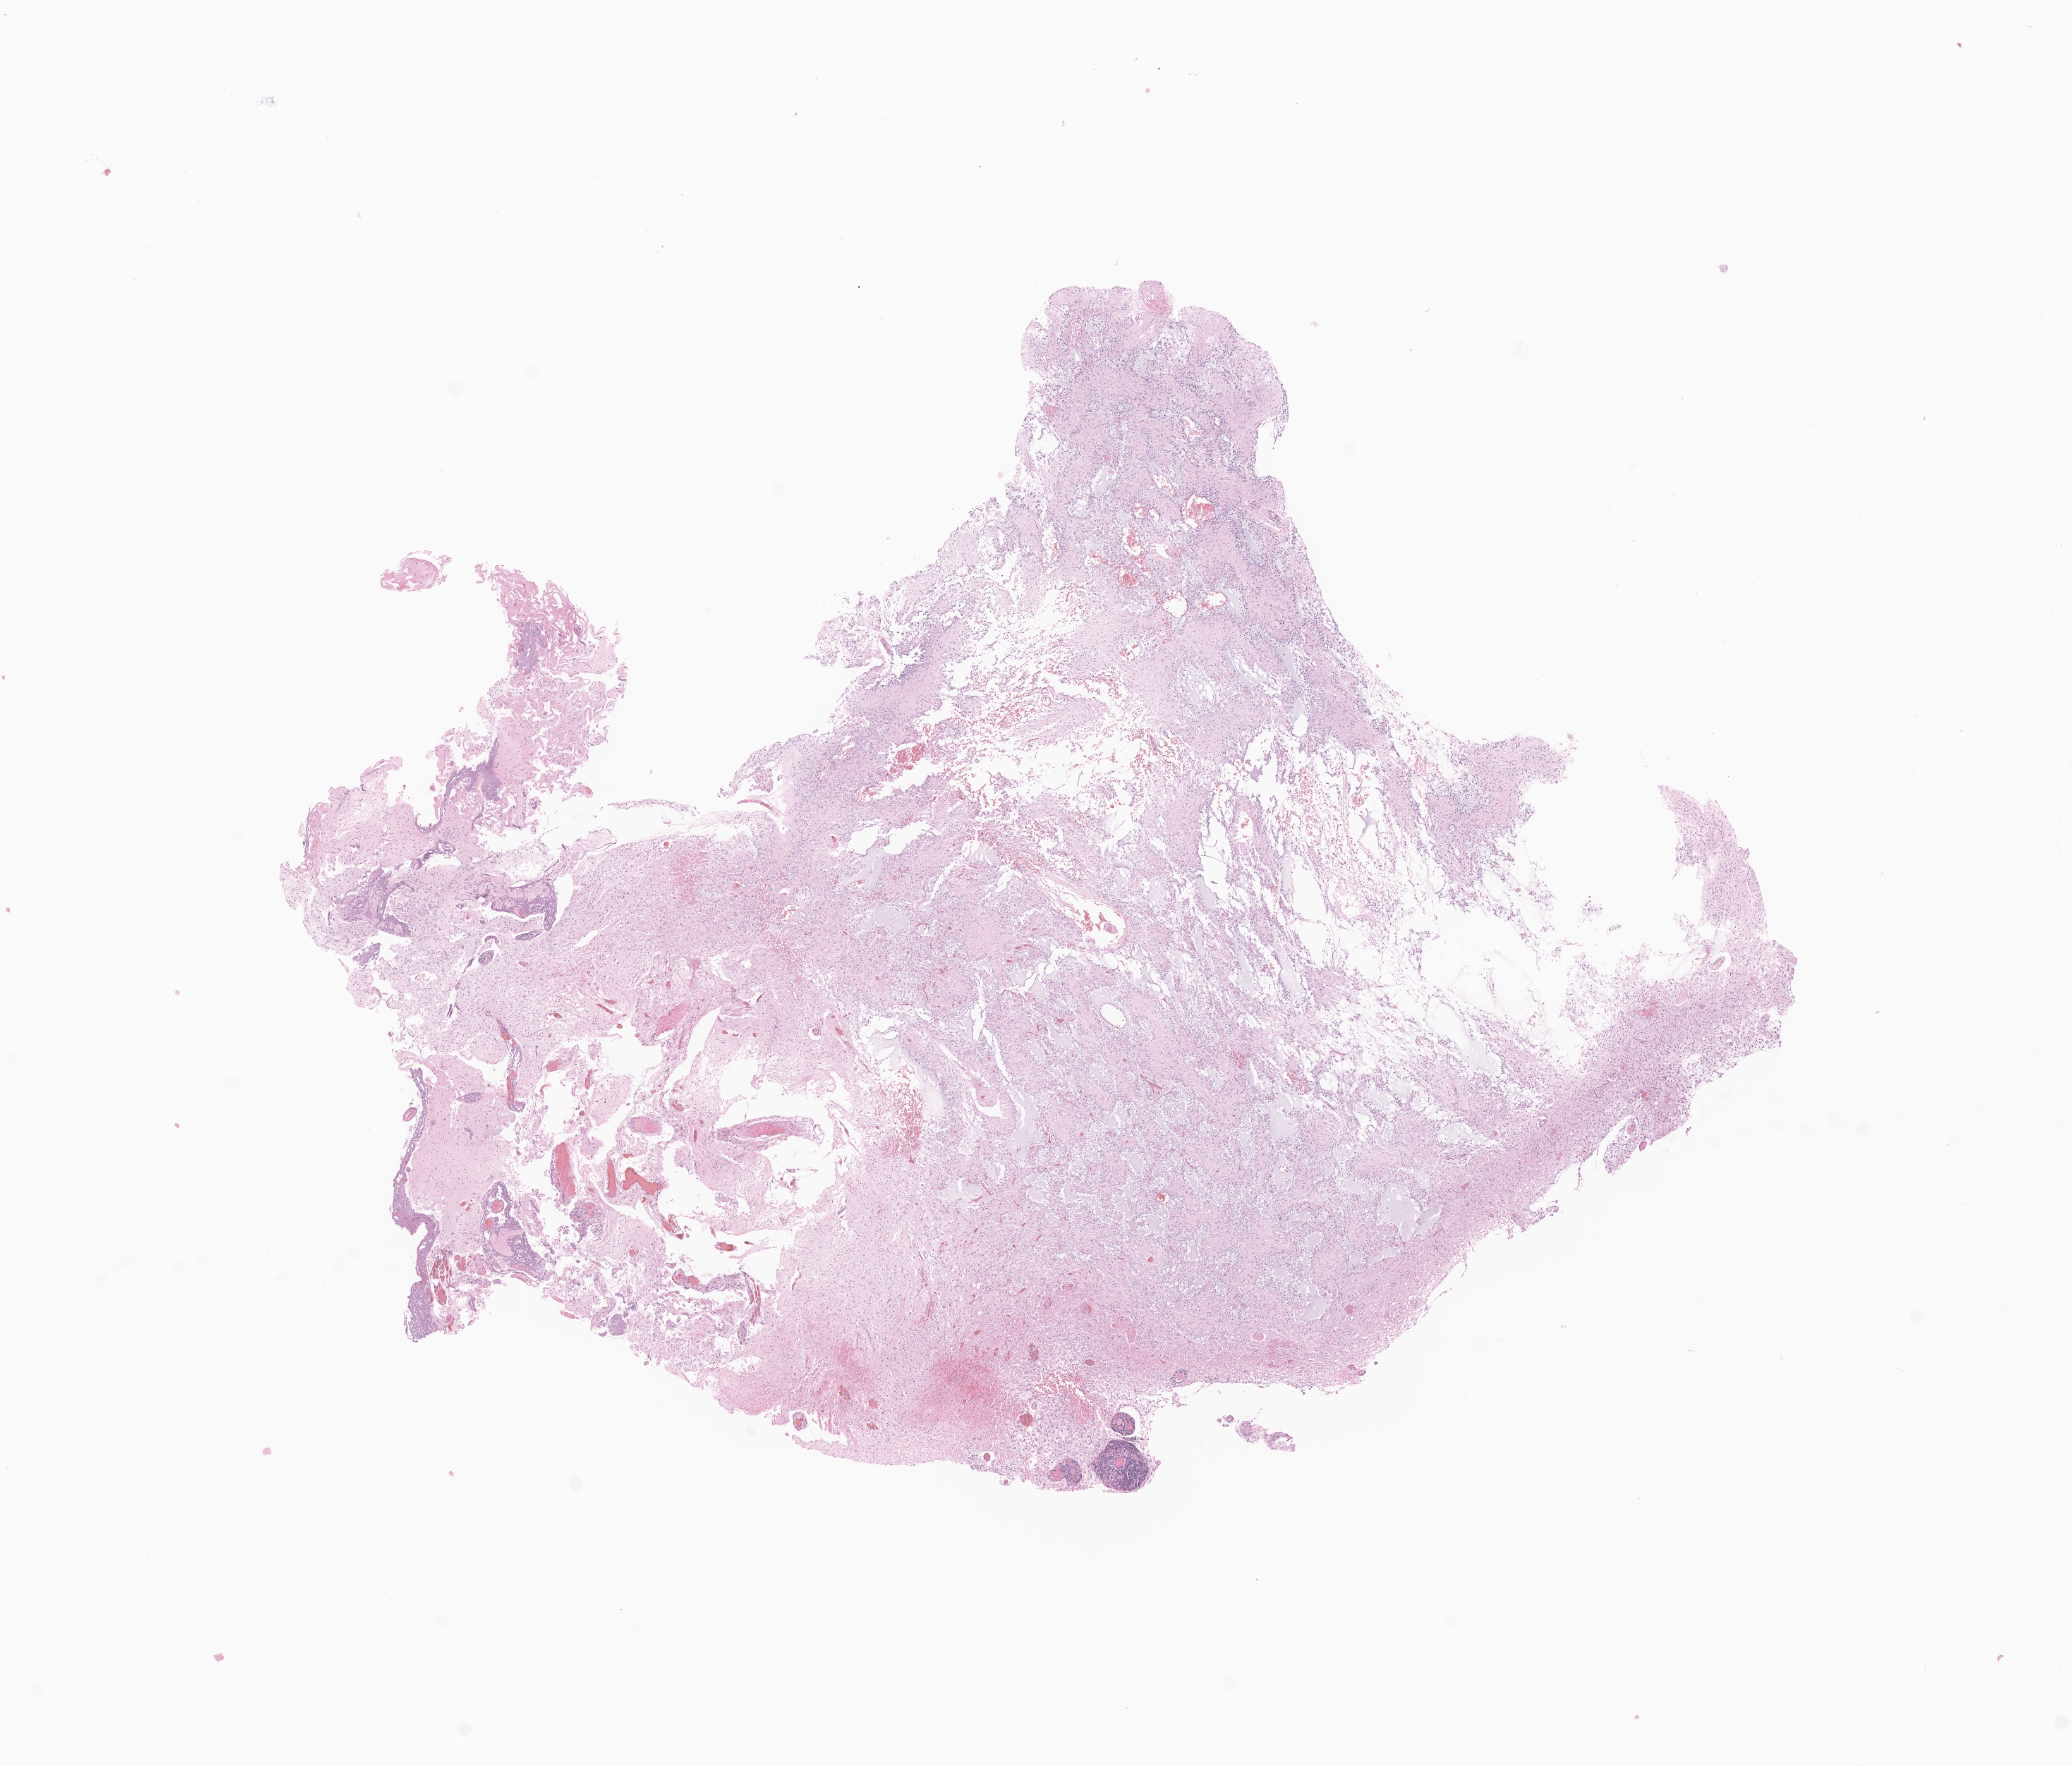
Digitized hematoxylin and eosin (H&E)-stained section of tumor tissue from the brain — shown as a low-resolution overview of the whole scanned area (about 13.8 x 11.8 mm). Formalin-fixed paraffin-embedded section. Patient female; age 141 months (11 years 9 months).
Recorded diagnosis: Neoplasm, uncertain whether benign or malignant.